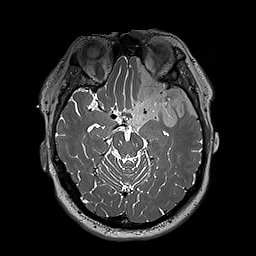
Brain MRI from a brain-tumour surgery series, one axial slice; slice 131 of 192 in the series (ordered by position); 256 × 256 image matrix. Case-level facts recorded for this patient, not image findings: histopathology: Oligodendroglioma; WHO grade: 3; IDH mutation: yes.
Outlined on this slice (outlined manually by an expert reader):
- tumour: bounding box (x1, y1, x2, y2) in pixels: (124, 59, 197, 131)